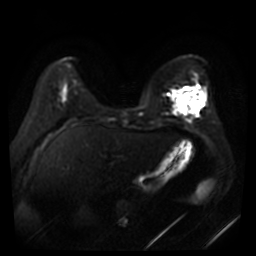
Breast MRI, one axial slice; position 13 of 44 along the scan axis; diffusion-weighted series; image 2 of 4 stored at this slice position (different b-values; order by instance number); 3 T; 5 mm slice thickness; 256 × 256 image matrix. Female patient.
Annotated regions visible in this slice (expert manual segmentation):
- tumour on diffusion-weighted imaging: bounding box [x1, y1, x2, y2] px = [177, 94, 195, 112]